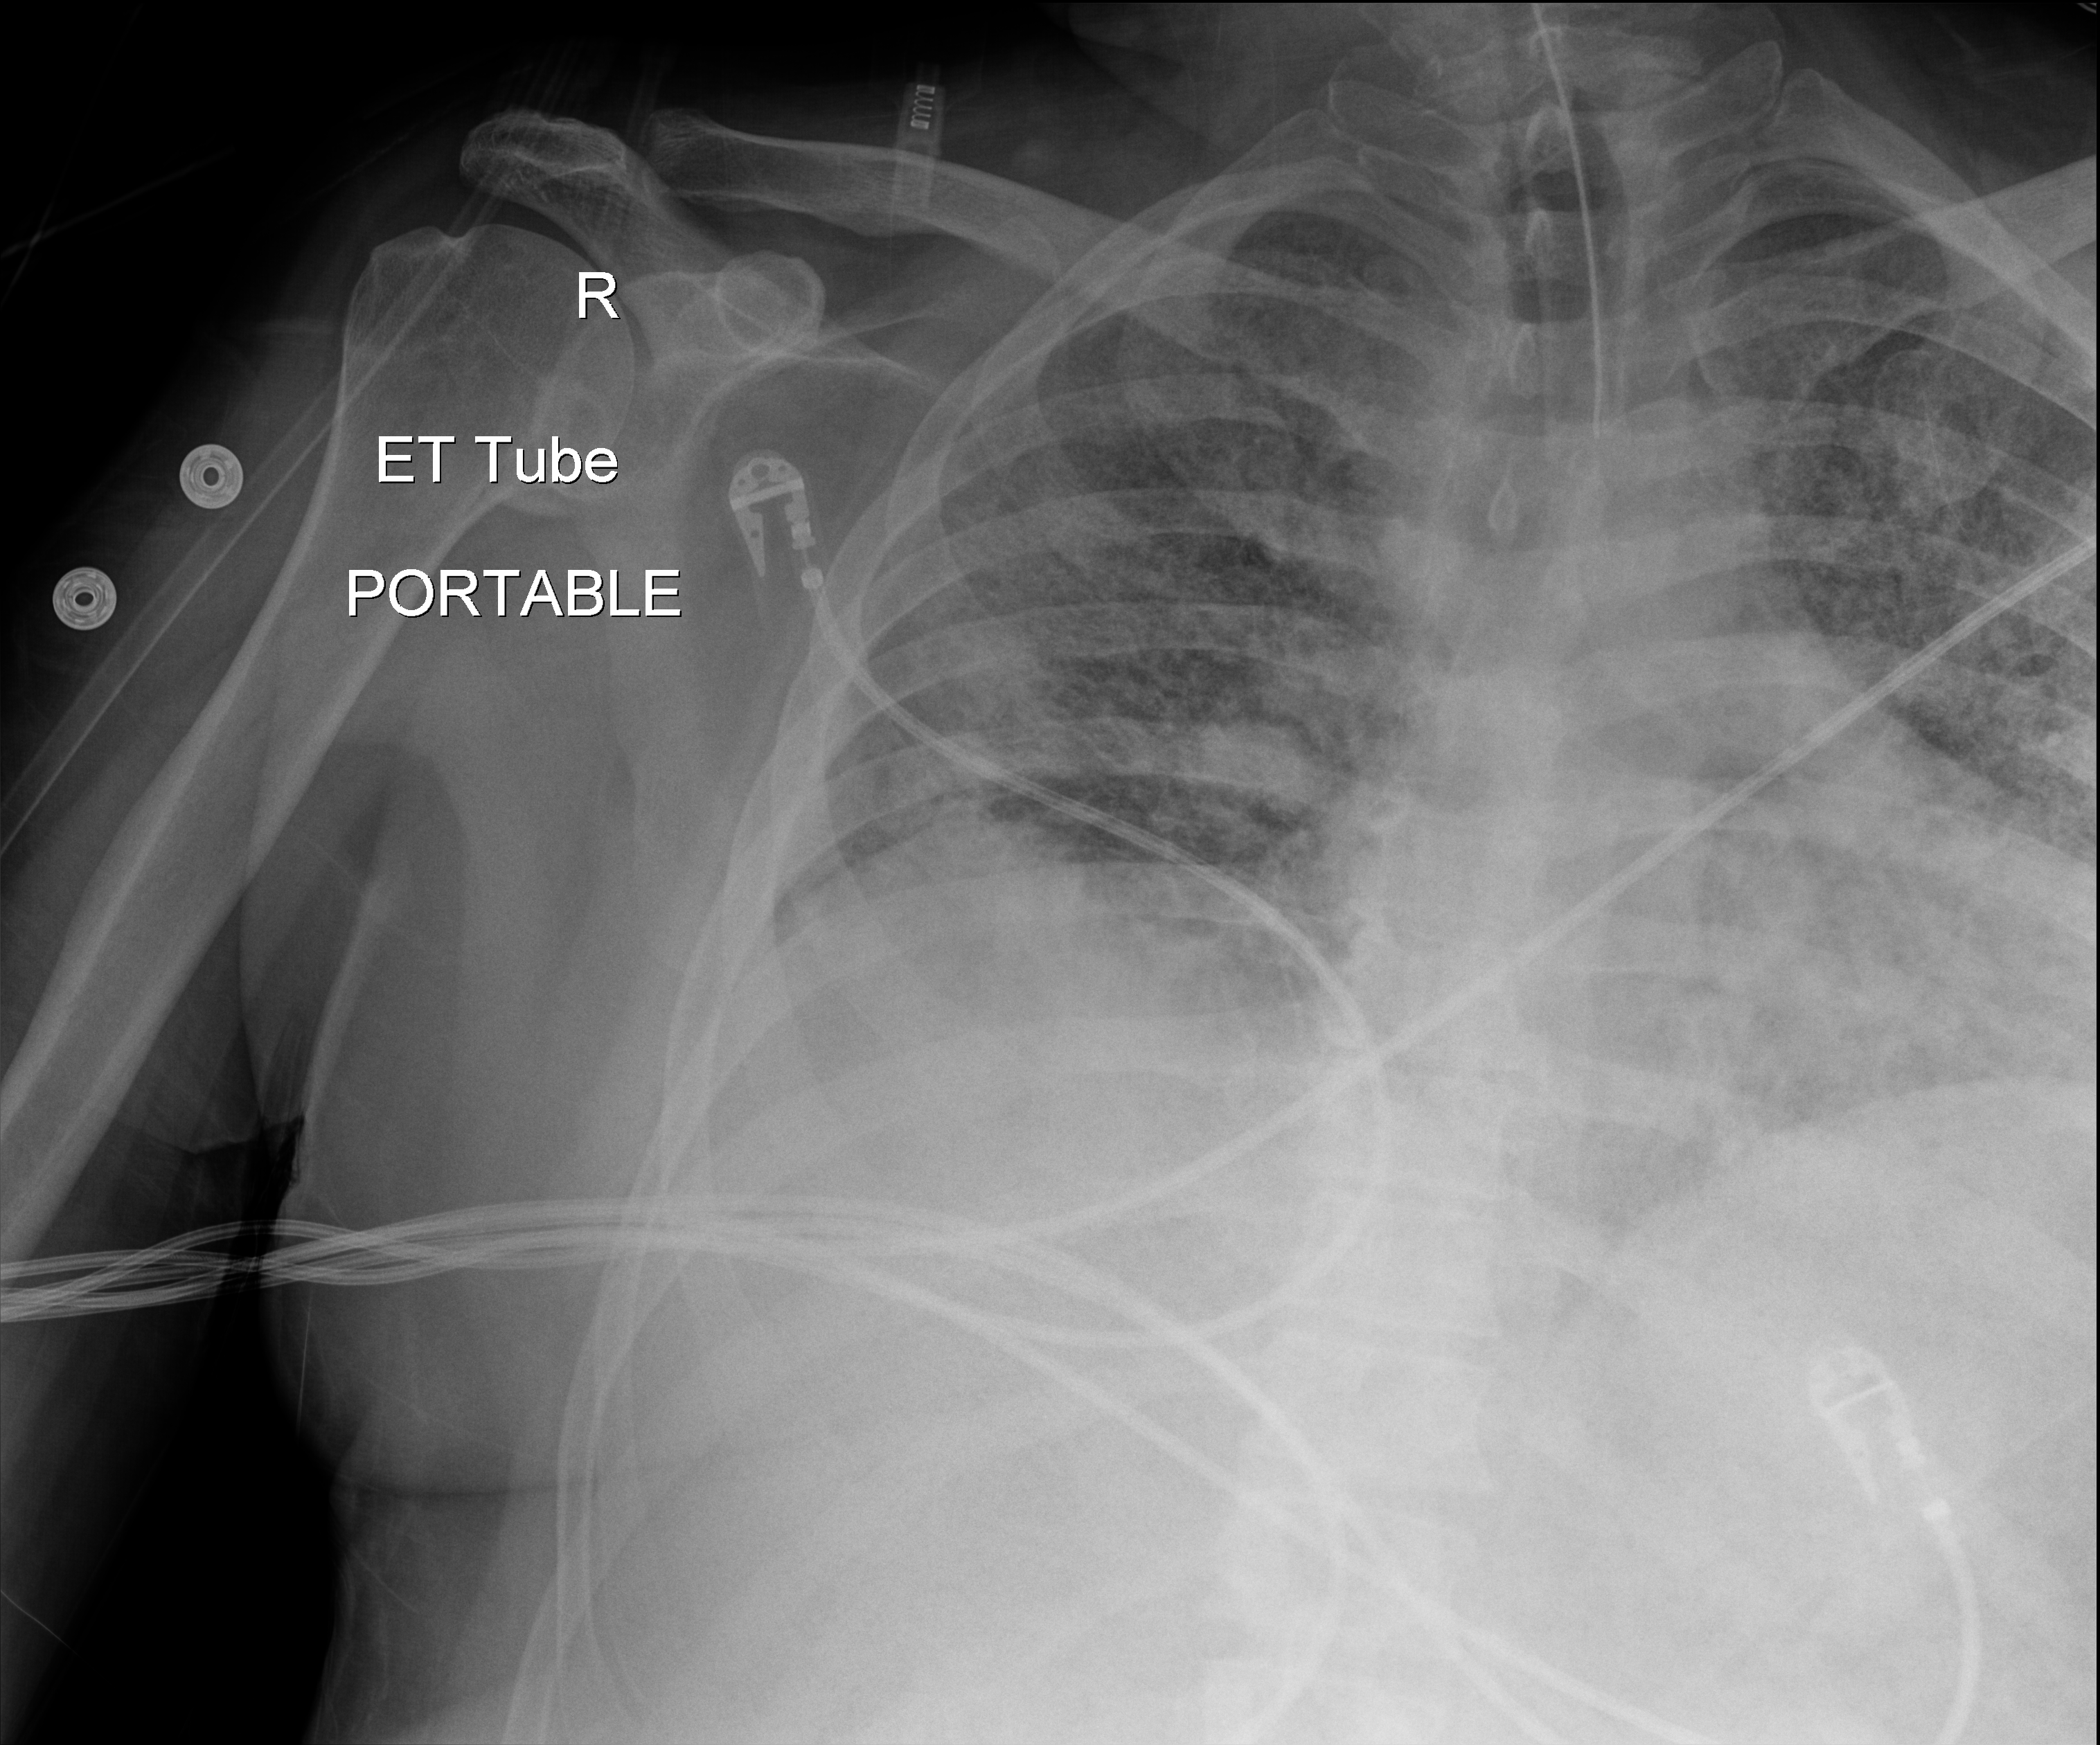
Chest X-ray. Patient hospitalised with COVID-19; male, aged 18–59 years.
Hospital-stay facts (about this admission, not read from this image; timing relative to this image not recorded): smoking status (admission record): never; admitted to intensive care during this hospital stay: yes; length of hospital stay: 80 days.